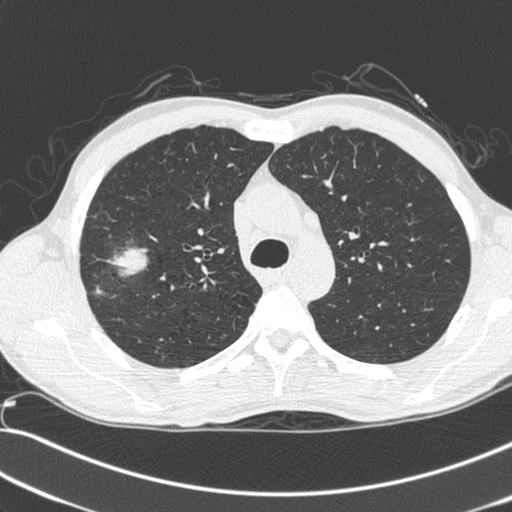
Axial slice from a low-dose chest CT screening exam, baseline annual screen, lung window (W 1500 / L -600 HU), slice 71 of 281 in the series, 512 × 512 image matrix. Male, age 55 years at enrolment. Current smoker at enrolment.
Lesion marked by an expert reader, bounding box (x1, y1, x2, y2) in pixels: (72, 237, 150, 308). Reader record for this screening exam (exam-level; its link to the box is not recorded): non-calcified nodule or mass ≥4 mm, right upper lobe, 52 × 39 mm, spiculated (stellate) margins, soft tissue attenuation. Later outcome: lung cancer diagnosed 25 days after this screen — large cell neuroendocrine carcinoma, right upper lobe, poorly differentiated (G3), stage IIB (AJCC 6th edition), 49 mm at pathology.